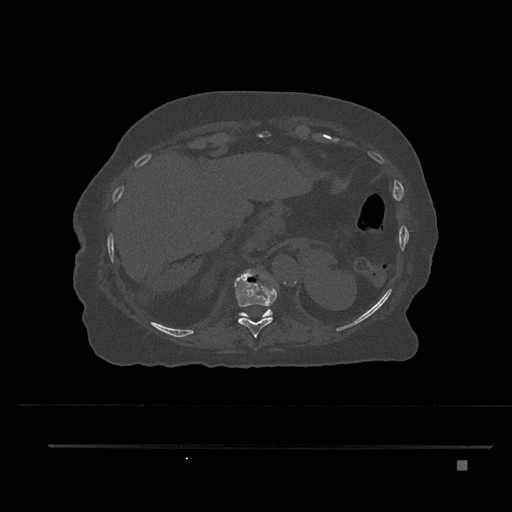
CT including the spine, one axial slice; slice 344 of 797 in the series (ordered by position); reconstruction kernel Br40s/3; 120 kVp; bone window (W 1800 / L 400 HU); 0.5 mm slice thickness; 512 × 512 image matrix, field of view 437 × 437 mm. Patient: female, 76 years. From the clinical record (not read from this slice): primary cancer: lung.
Structures marked on this image (semi-automatically segmented with operator editing):
- T10 vertebra: bounding box [x1, y1, x2, y2] px = [235, 272, 277, 337]
- T11 vertebra: [239, 309, 273, 319]